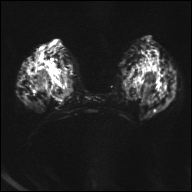
Breast MRI, one axial slice. Position 18 of 32 along the scan axis. Diffusion-weighted series; image 2 of 4 stored at this slice position (different b-values; order by instance number). 1.5 T. 192 × 192 image matrix, field of view 360 × 360 mm. Female patient.
Outlined on this slice (expert manual segmentation):
- tumour on diffusion-weighted imaging: bounding box (x1, y1, x2, y2) in pixels: (35, 69, 74, 97)